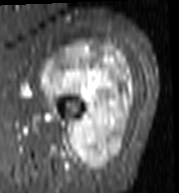
MRI of an extremity soft-tissue mass, one axial slice; STIR; MR volume resampled by the dataset authors to the PET/CT grid (not the native acquisition matrix); 3.27 mm slice thickness; 179 × 193 image matrix, field of view 175 × 188 mm. Female patient. From the clinical record (not read from this slice): histological type: undifferentiated – high grade; grade: high; site of the primary tumour: left thigh.
Outlined on this slice (expert contour drawn on MRI and transferred to this co-registered scan by the dataset authors):
- gross tumour volume including surrounding oedema: bounding box <41,41,135,170> (left, top, right, bottom; pixels)
- gross tumour volume (mass): <41,41,135,170>